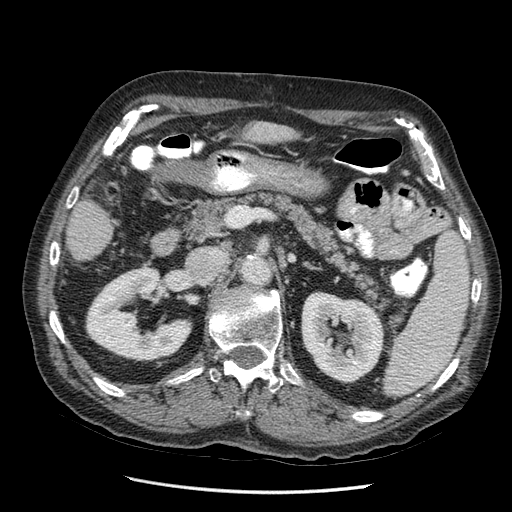
Contrast-enhanced abdominal CT (liver protocol), one axial slice; position 13 of 67 along the scan axis; reconstruction kernel STANDARD; soft-tissue window (W 400 / L 40 HU); 512 × 512 image matrix, field of view 360 × 360 mm. From the clinical record (not read from this slice): diagnosis: hepatocellular carcinoma (patient treated with transarterial chemoembolisation; whether this scan precedes or follows treatment is not stated here); TNM stage (as recorded): Stage-I; Child-Pugh class: A; tumour differentiation: moderately differentiated; tumour nodularity: uninodular.
Structures marked on this image (semi-automatically segmented with operator editing):
- liver parenchyma outside the tumour (the mass and vessels are separate outlines, so this box may not span the whole liver): box from (x=220, y=118) to (x=309, y=152) px